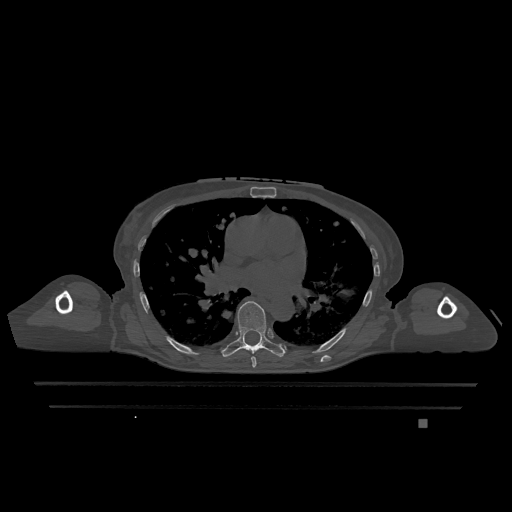
CT including the spine, one axial slice. Slice 749 of 1317 in the series (ordered by position). Bone window (W 1800 / L 400 HU). 0.5 mm slice thickness. 512 × 512 image matrix, field of view 500 × 500 mm. Female patient, age 74 years. From the clinical record (not read from this slice): primary cancer: lung.
Outlined on this slice (semi-automatic segmentation, software-assisted and operator-edited):
- T6 vertebra: box from (x=251, y=356) to (x=257, y=368) px
- T7 vertebra: (x=221, y=301)–(x=286, y=357)